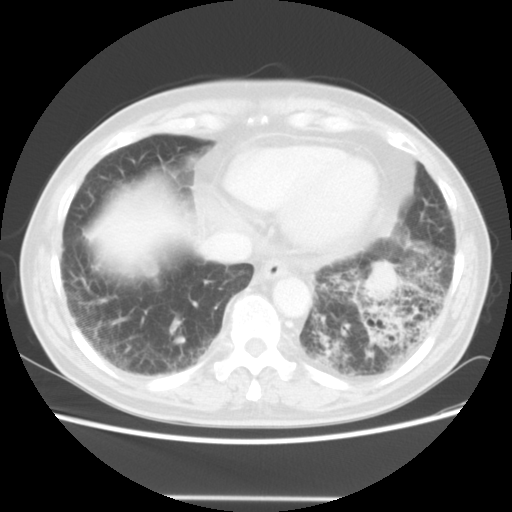
Chest CT, one axial slice. Position 12 of 56 along the scan axis. 140 kVp. Lung window (W 1500 / L -600 HU). 5 mm slice thickness. 512 × 512 image matrix. Male patient, age 66 years. From the clinical record (not read from this slice): clinical TNM (as recorded): T4 N3 M0; histopathological grade: G3.
Annotated regions visible in this slice (rectangle marked by the reading radiologist):
- lung tumour (recorded histology: small cell carcinoma): bounding box <352,256,406,312> (left, top, right, bottom; pixels)